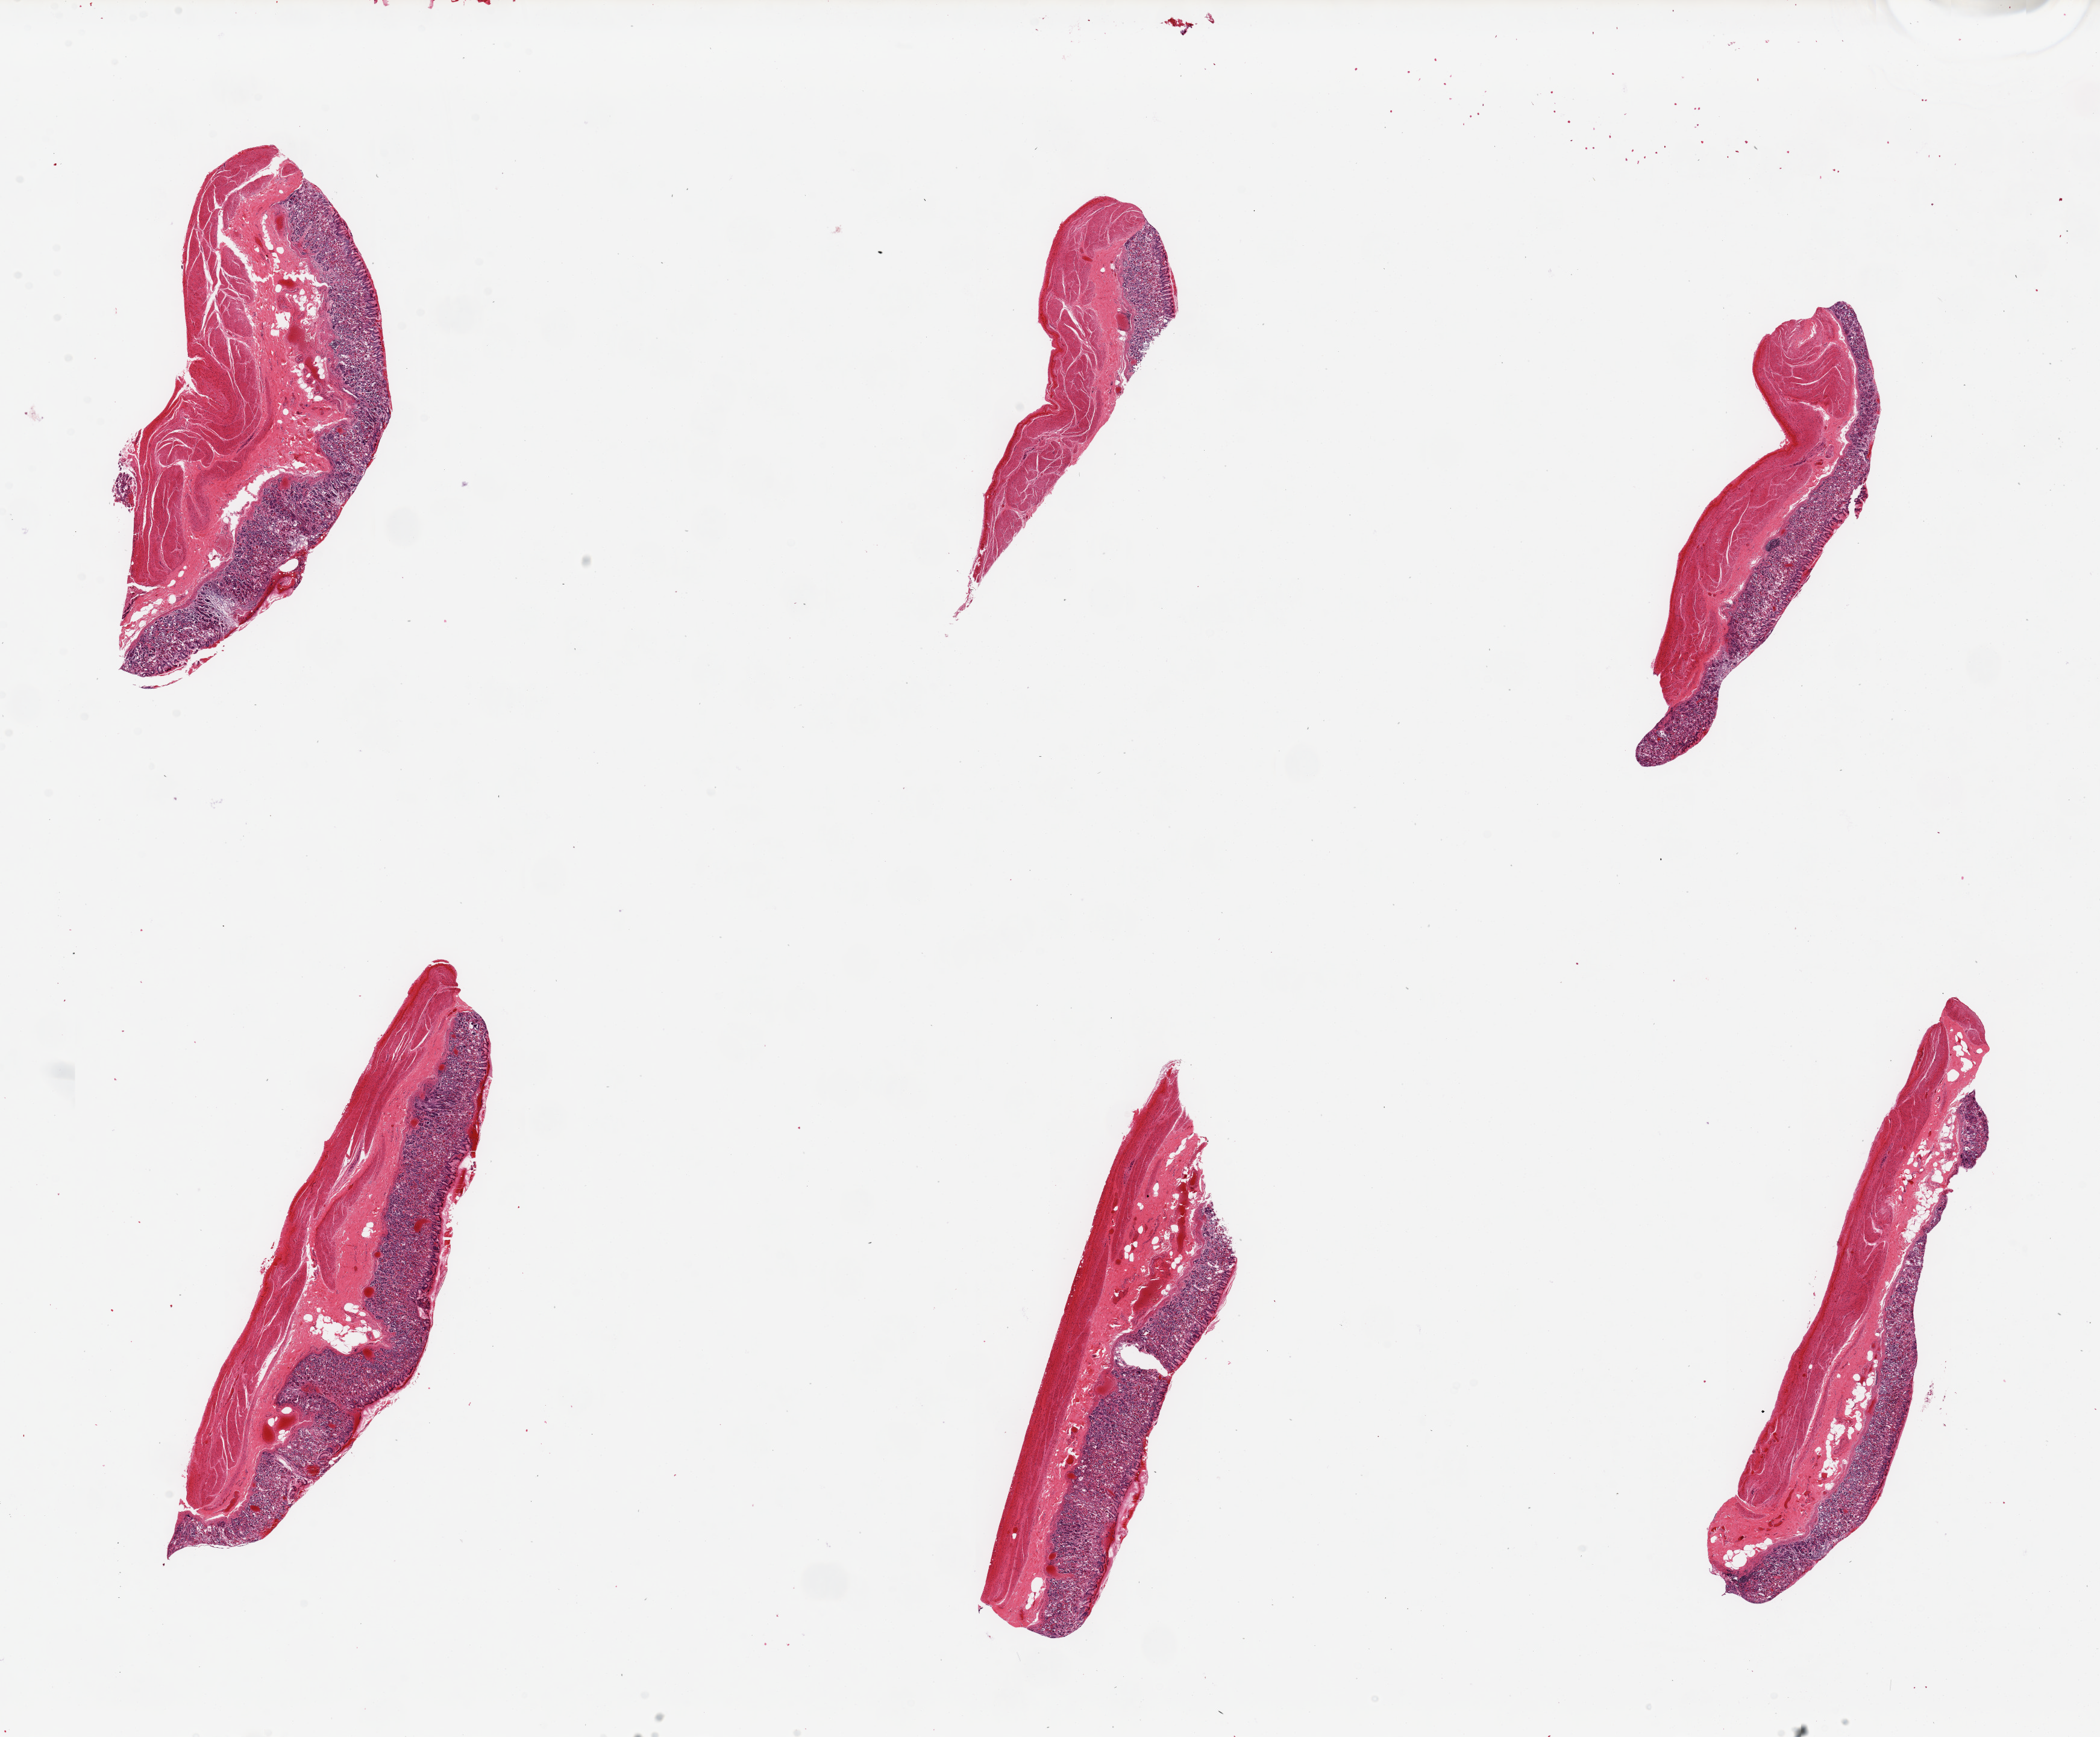
Whole-slide image, hematoxylin and eosin (H&E) stain, brightfield — shown as a low-resolution overview of the whole scanned area (about 27.6 x 22.8 mm, acquisition: 20x scan); PAXgene-fixed paraffin-embedded (PFPE) section; sampled site (target tissue): stomach; donor tissue sample.
- review note (as recorded): 6 pieces ~6x2.5mm. Mucosa variably well-poorly preserved, up to 30-40 thickness, ~700 microns